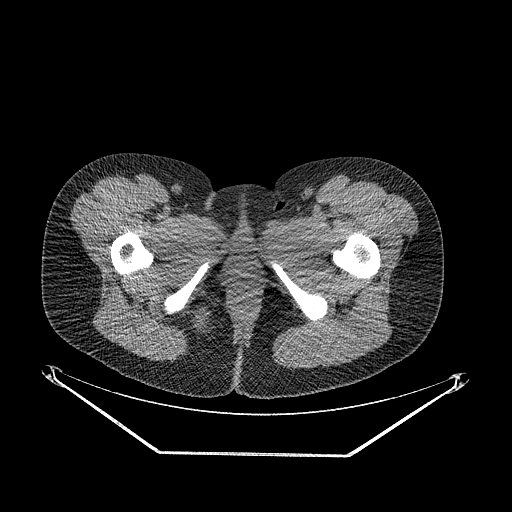
CT of an extremity soft-tissue mass (from a PET/CT study), one axial slice. Slice 33 of 267 in the series (ordered by position). Soft-tissue window (W 400 / L 40 HU). 3.75 mm slice thickness. 512 × 512 image matrix, field of view 500 × 500 mm. Female patient. Case-level facts recorded for this patient, not image findings: histological type: epithelioid sarcoma; grade: intermediate; site of the primary tumour: right buttock.
Outlined on this slice (expert contour drawn on MRI and transferred to this co-registered scan by the dataset authors):
- gross tumour volume including surrounding oedema: bounding box [x1, y1, x2, y2] px = [180, 297, 220, 346]
- gross tumour volume (mass): [183, 304, 213, 341]